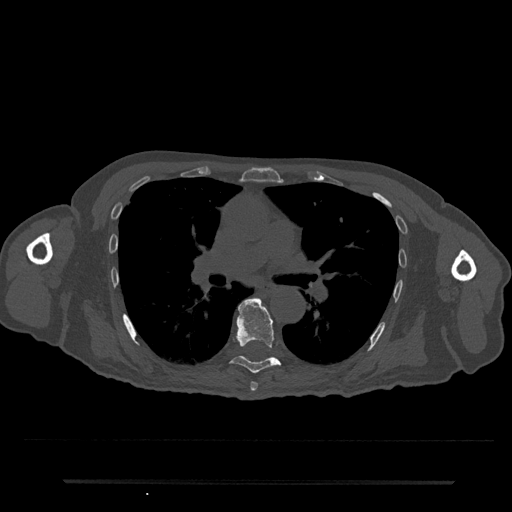
CT including the spine, one axial slice. Slice 482 of 797 in the series (ordered by position). Reconstruction kernel Br40s/3. 120 kVp. Bone window (W 1800 / L 400 HU). 0.5 mm slice thickness. 512 × 512 image matrix. Male patient, age 74 years. Case-level facts recorded for this patient, not image findings: primary cancer: prostate.
Outlined on this slice (semi-automatic segmentation, software-assisted and operator-edited):
- T6 vertebra: box from (x=250, y=382) to (x=258, y=392) px
- T7 vertebra: (x=231, y=298)–(x=280, y=374)